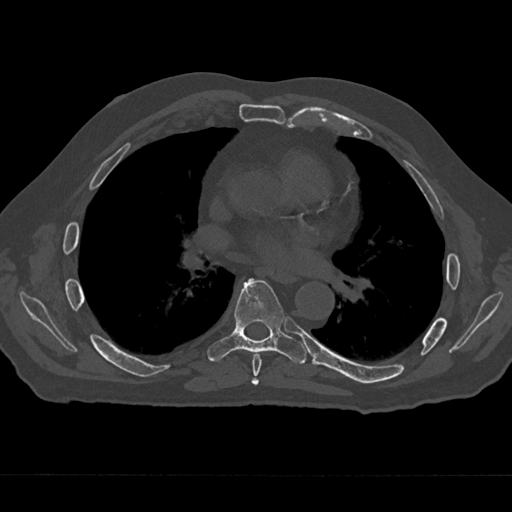
CT including the spine, one axial slice. Position 381 of 797 along the scan axis. 120 kVp. Bone window (W 1800 / L 400 HU). 0.5 mm slice thickness. 512 × 512 image matrix. Patient: male, 75 years. From the clinical record (not read from this slice): primary cancer: renal; vertebrae with lytic lesions (as recorded): T4.
Annotated regions visible in this slice (semi-automatically segmented with operator editing):
- T6 vertebra: bounding box <252,353,262,385> (left, top, right, bottom; pixels)
- T7 vertebra: <207,278,307,364>